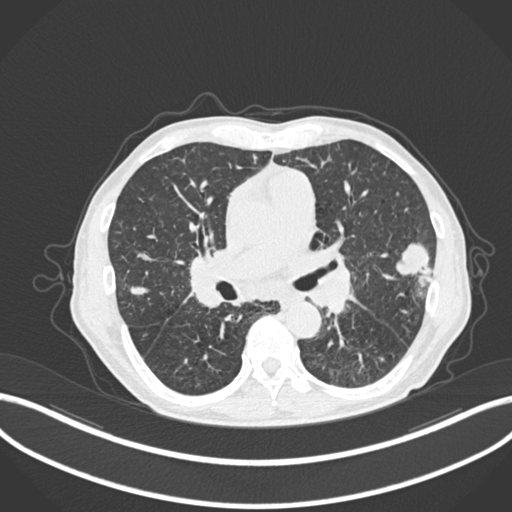
Chest CT, one axial slice; slice 127 of 287 in the series (ordered by position); 120 kVp; lung window (W 1500 / L -600 HU); 512 × 512 image matrix, field of view 400 × 400 mm. Patient: male, 74 years. Case-level facts recorded for this patient, not image findings: clinical TNM (as recorded): T2a N1 M0.
Outlined on this slice (bounding box drawn by a radiologist):
- lung tumour (recorded histology: adenocarcinoma): box from (x=397, y=239) to (x=432, y=289) px